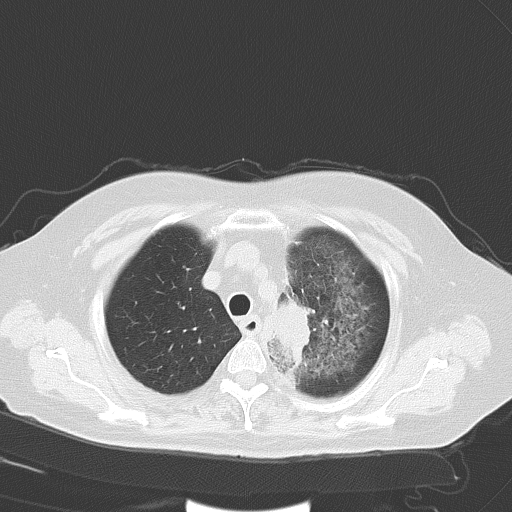
Chest CT, one axial slice; slice 45 of 56 in the series (ordered by position); lung window (W 1500 / L -600 HU); 5 mm slice thickness; 512 × 512 image matrix, field of view 353 × 353 mm. Patient: female, 65 years. Case-level facts recorded for this patient, not image findings: clinical TNM (as recorded): T2b N1 M0.
Annotated regions visible in this slice (bounding box drawn by a radiologist):
- lung tumour (recorded histology: adenocarcinoma): bounding box <274,294,316,368> (left, top, right, bottom; pixels)